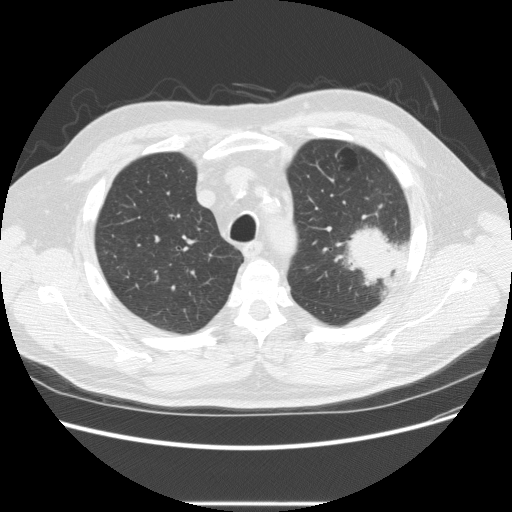
Low-dose screening chest CT, one axial slice. Position 178 of 233 along the scan axis. Reconstruction kernel STANDARD. 120 kVp. Lung window (W 1500 / L -600 HU). 2.5 mm slice thickness. 512 × 512 image matrix.
Outlined on this slice (outlined manually by an expert reader):
- lesion 1 (tumor, upper lobe of left lung): box from (x=346, y=226) to (x=401, y=288) px